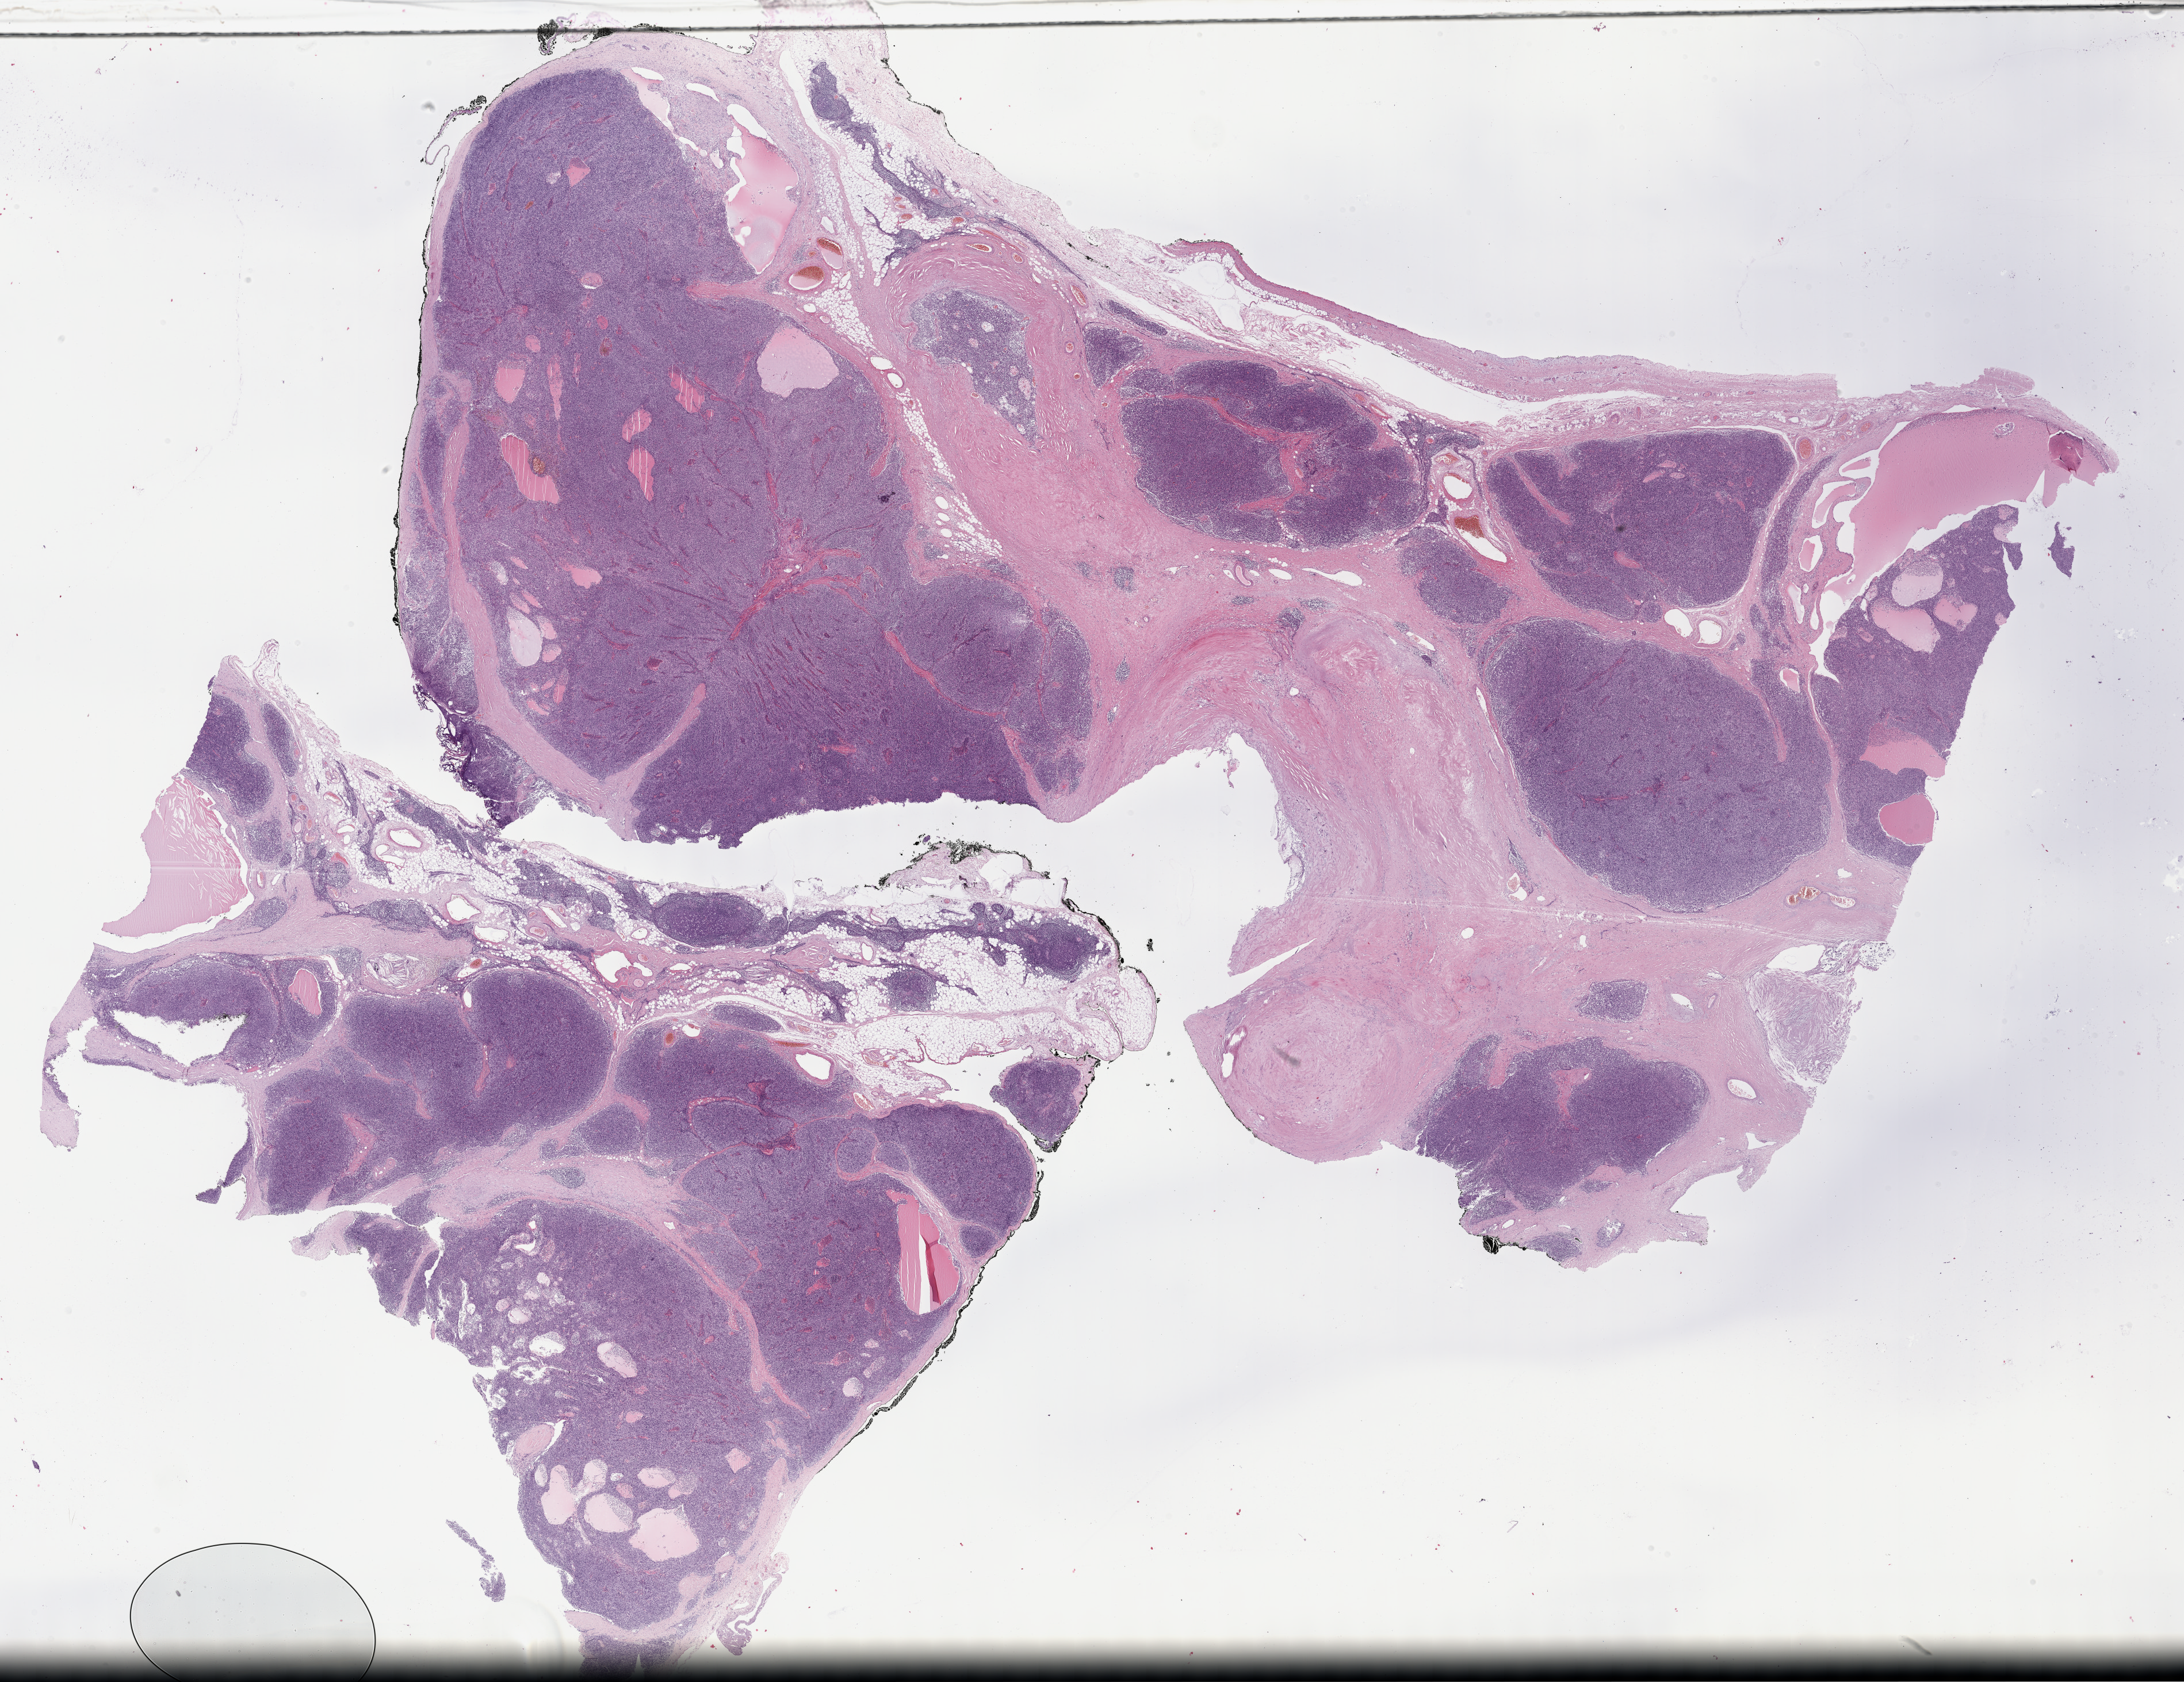
Hematoxylin and eosin (H&E) stained whole-slide image — low-resolution overview of the scanned area, about 30.7 x 23.7 mm. Formalin-fixed paraffin-embedded (FFPE) diagnostic section. Thymus, primary tumour sample. Male, age 39 years at initial diagnosis.
Diagnosis: Thymoma, type B2, malignant (anterior mediastinum).